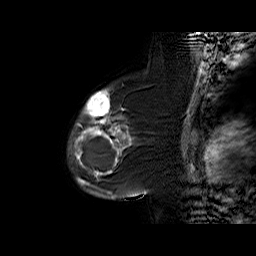
Breast MRI (dynamic contrast-enhanced), one sagittal slice; position 45 of 60 along the scan axis; dynamic contrast-enhanced series, time point 2 of 6 at this slice position (early post-contrast); 1.5 T; TE 6.3 ms, TR 32.4 ms; 4 mm slice thickness; 256 × 256 image matrix, field of view 200 × 200 mm. Female patient. Case-level facts recorded for this patient, not image findings: setting: breast cancer imaged before/during neoadjuvant chemotherapy; receptor status: triple-negative.
Outlined on this slice (semi-automatic segmentation, software-assisted and operator-edited):
- analysis volume of interest (the breast-tissue region the enhancement analysis was run in; not a lesion): bounding box [x1, y1, x2, y2] px = [67, 88, 136, 187]
- tumour enhancement mask (voxels above the 100 % enhancement threshold inside the analysis volume of interest): [73, 89, 130, 184]